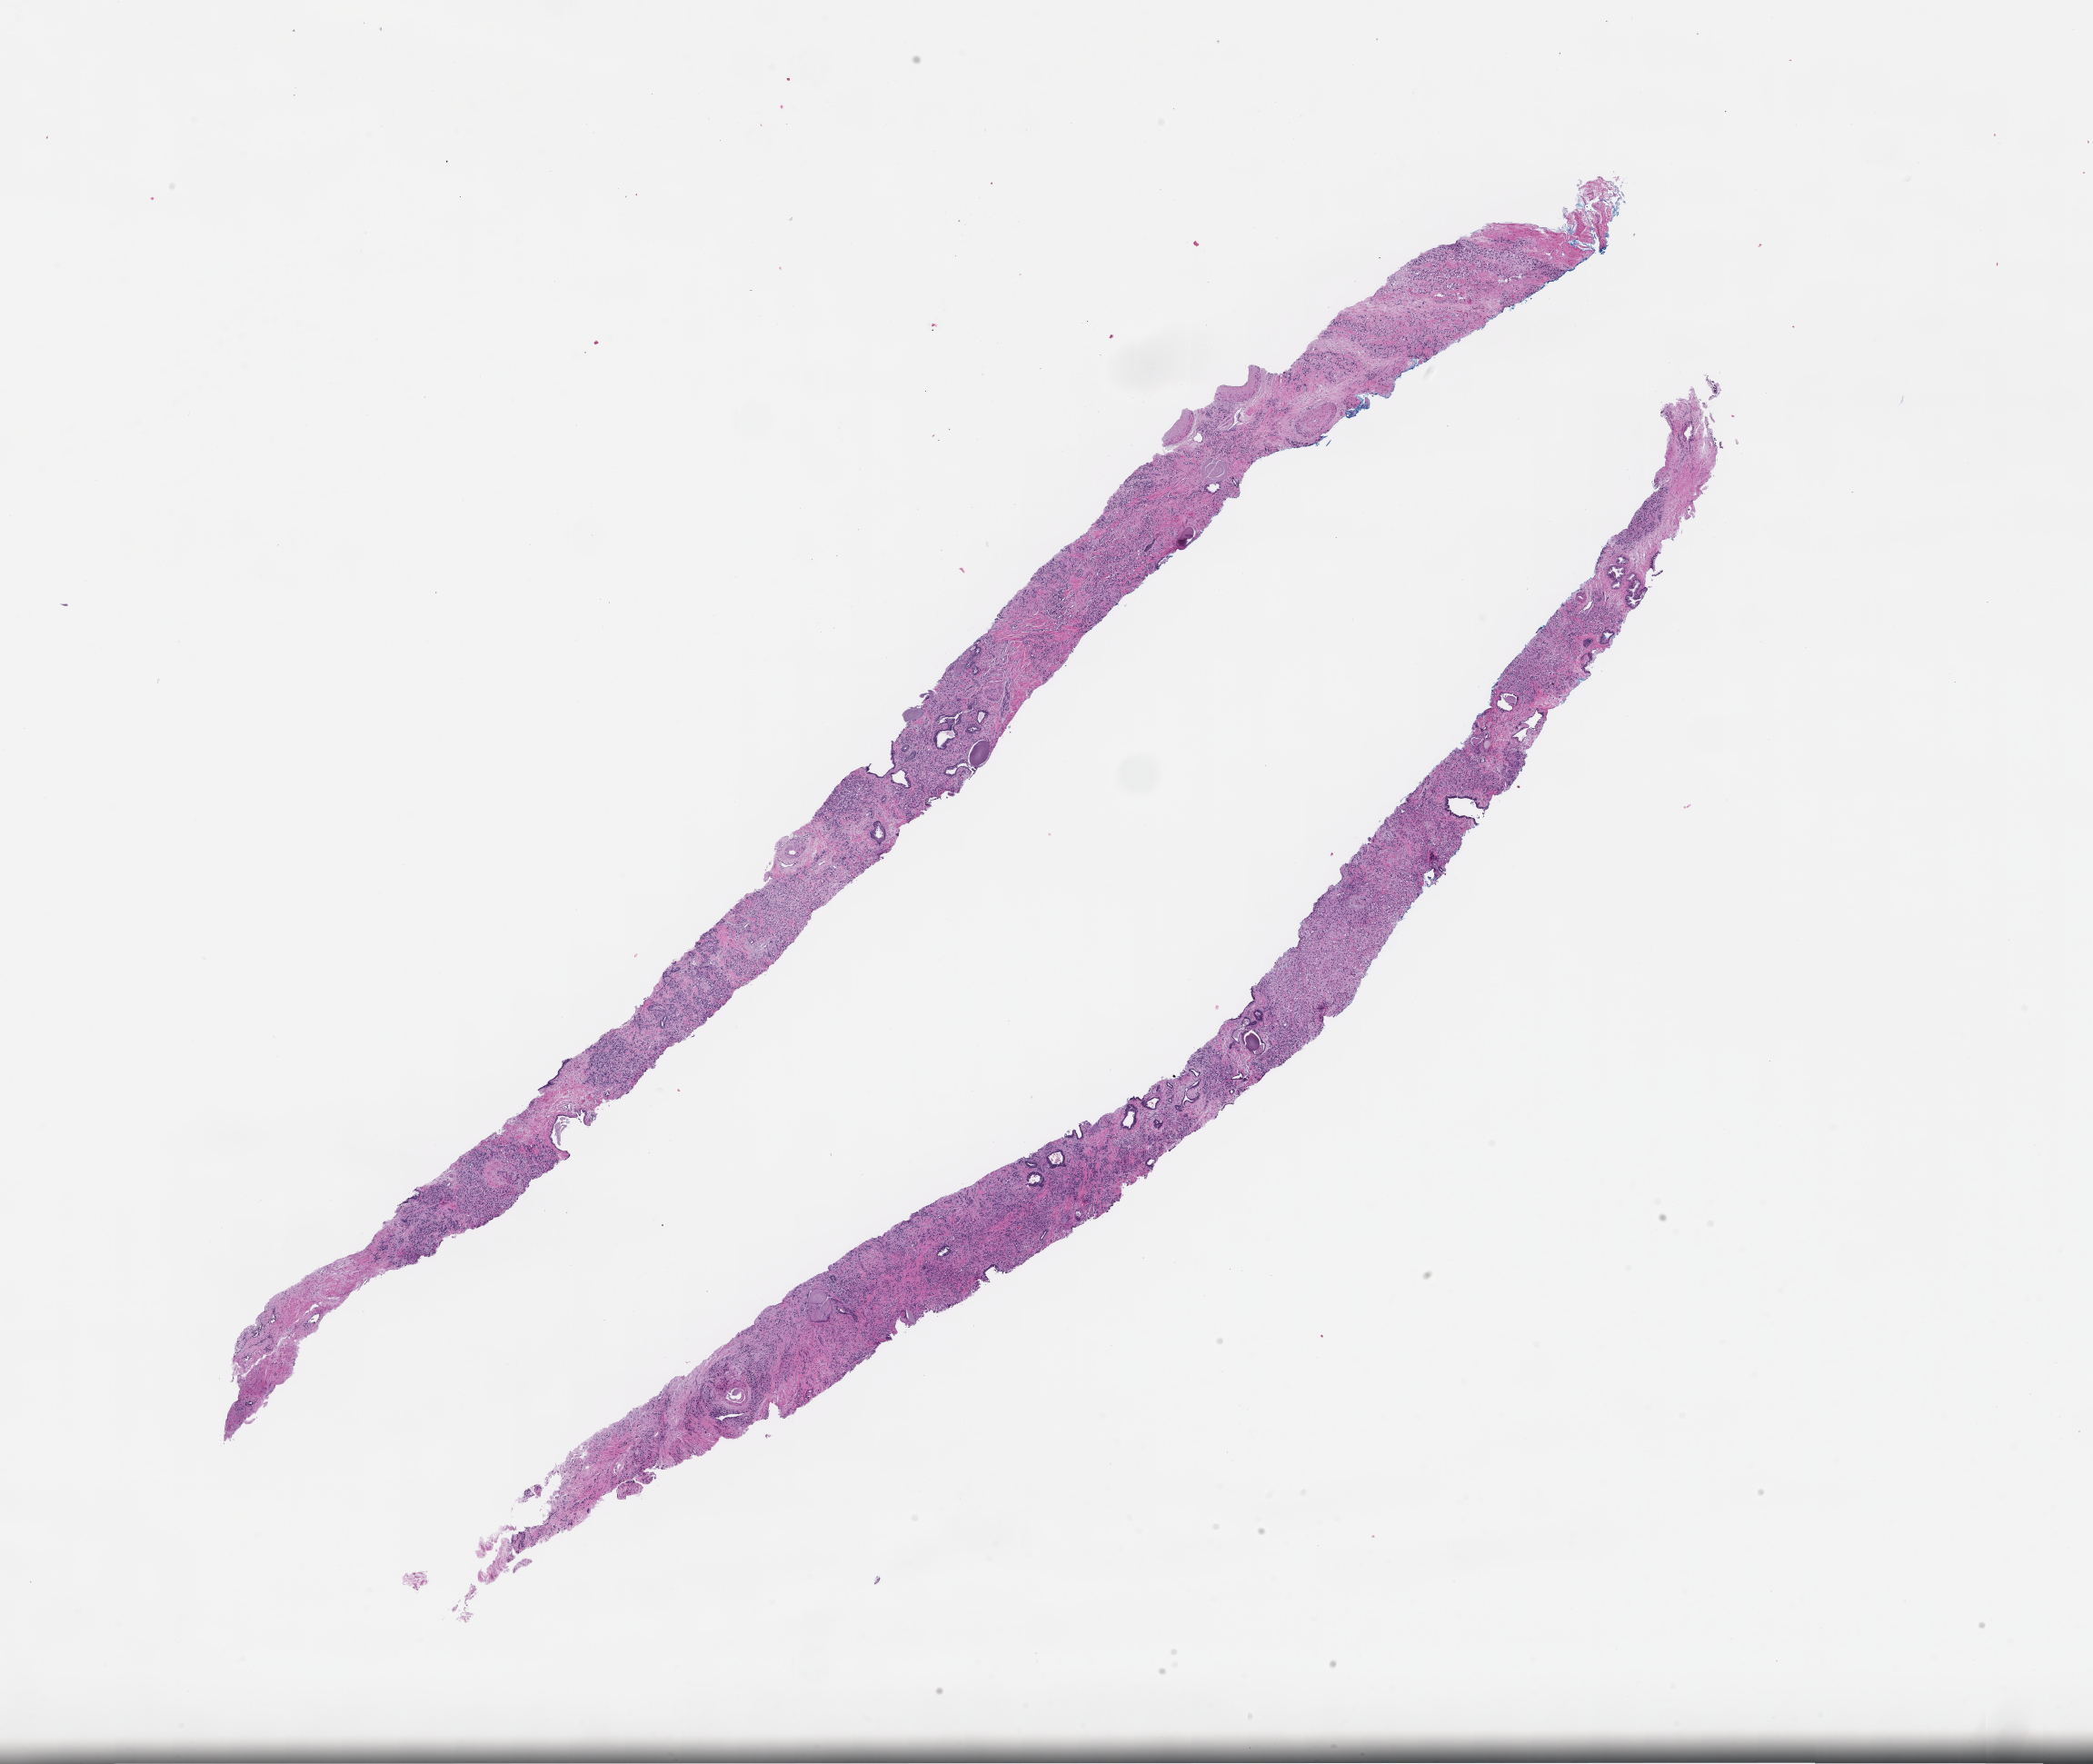
Haematoxylin and eosin whole-slide image — low-resolution overview of the scanned area, about 18.6 x 15.7 mm. FFPE section. Tissue site: prostate. Archival tissue. Patient sex: male.
* this section: primary tumour tissue
* diagnosis: Prostate Carcinoma